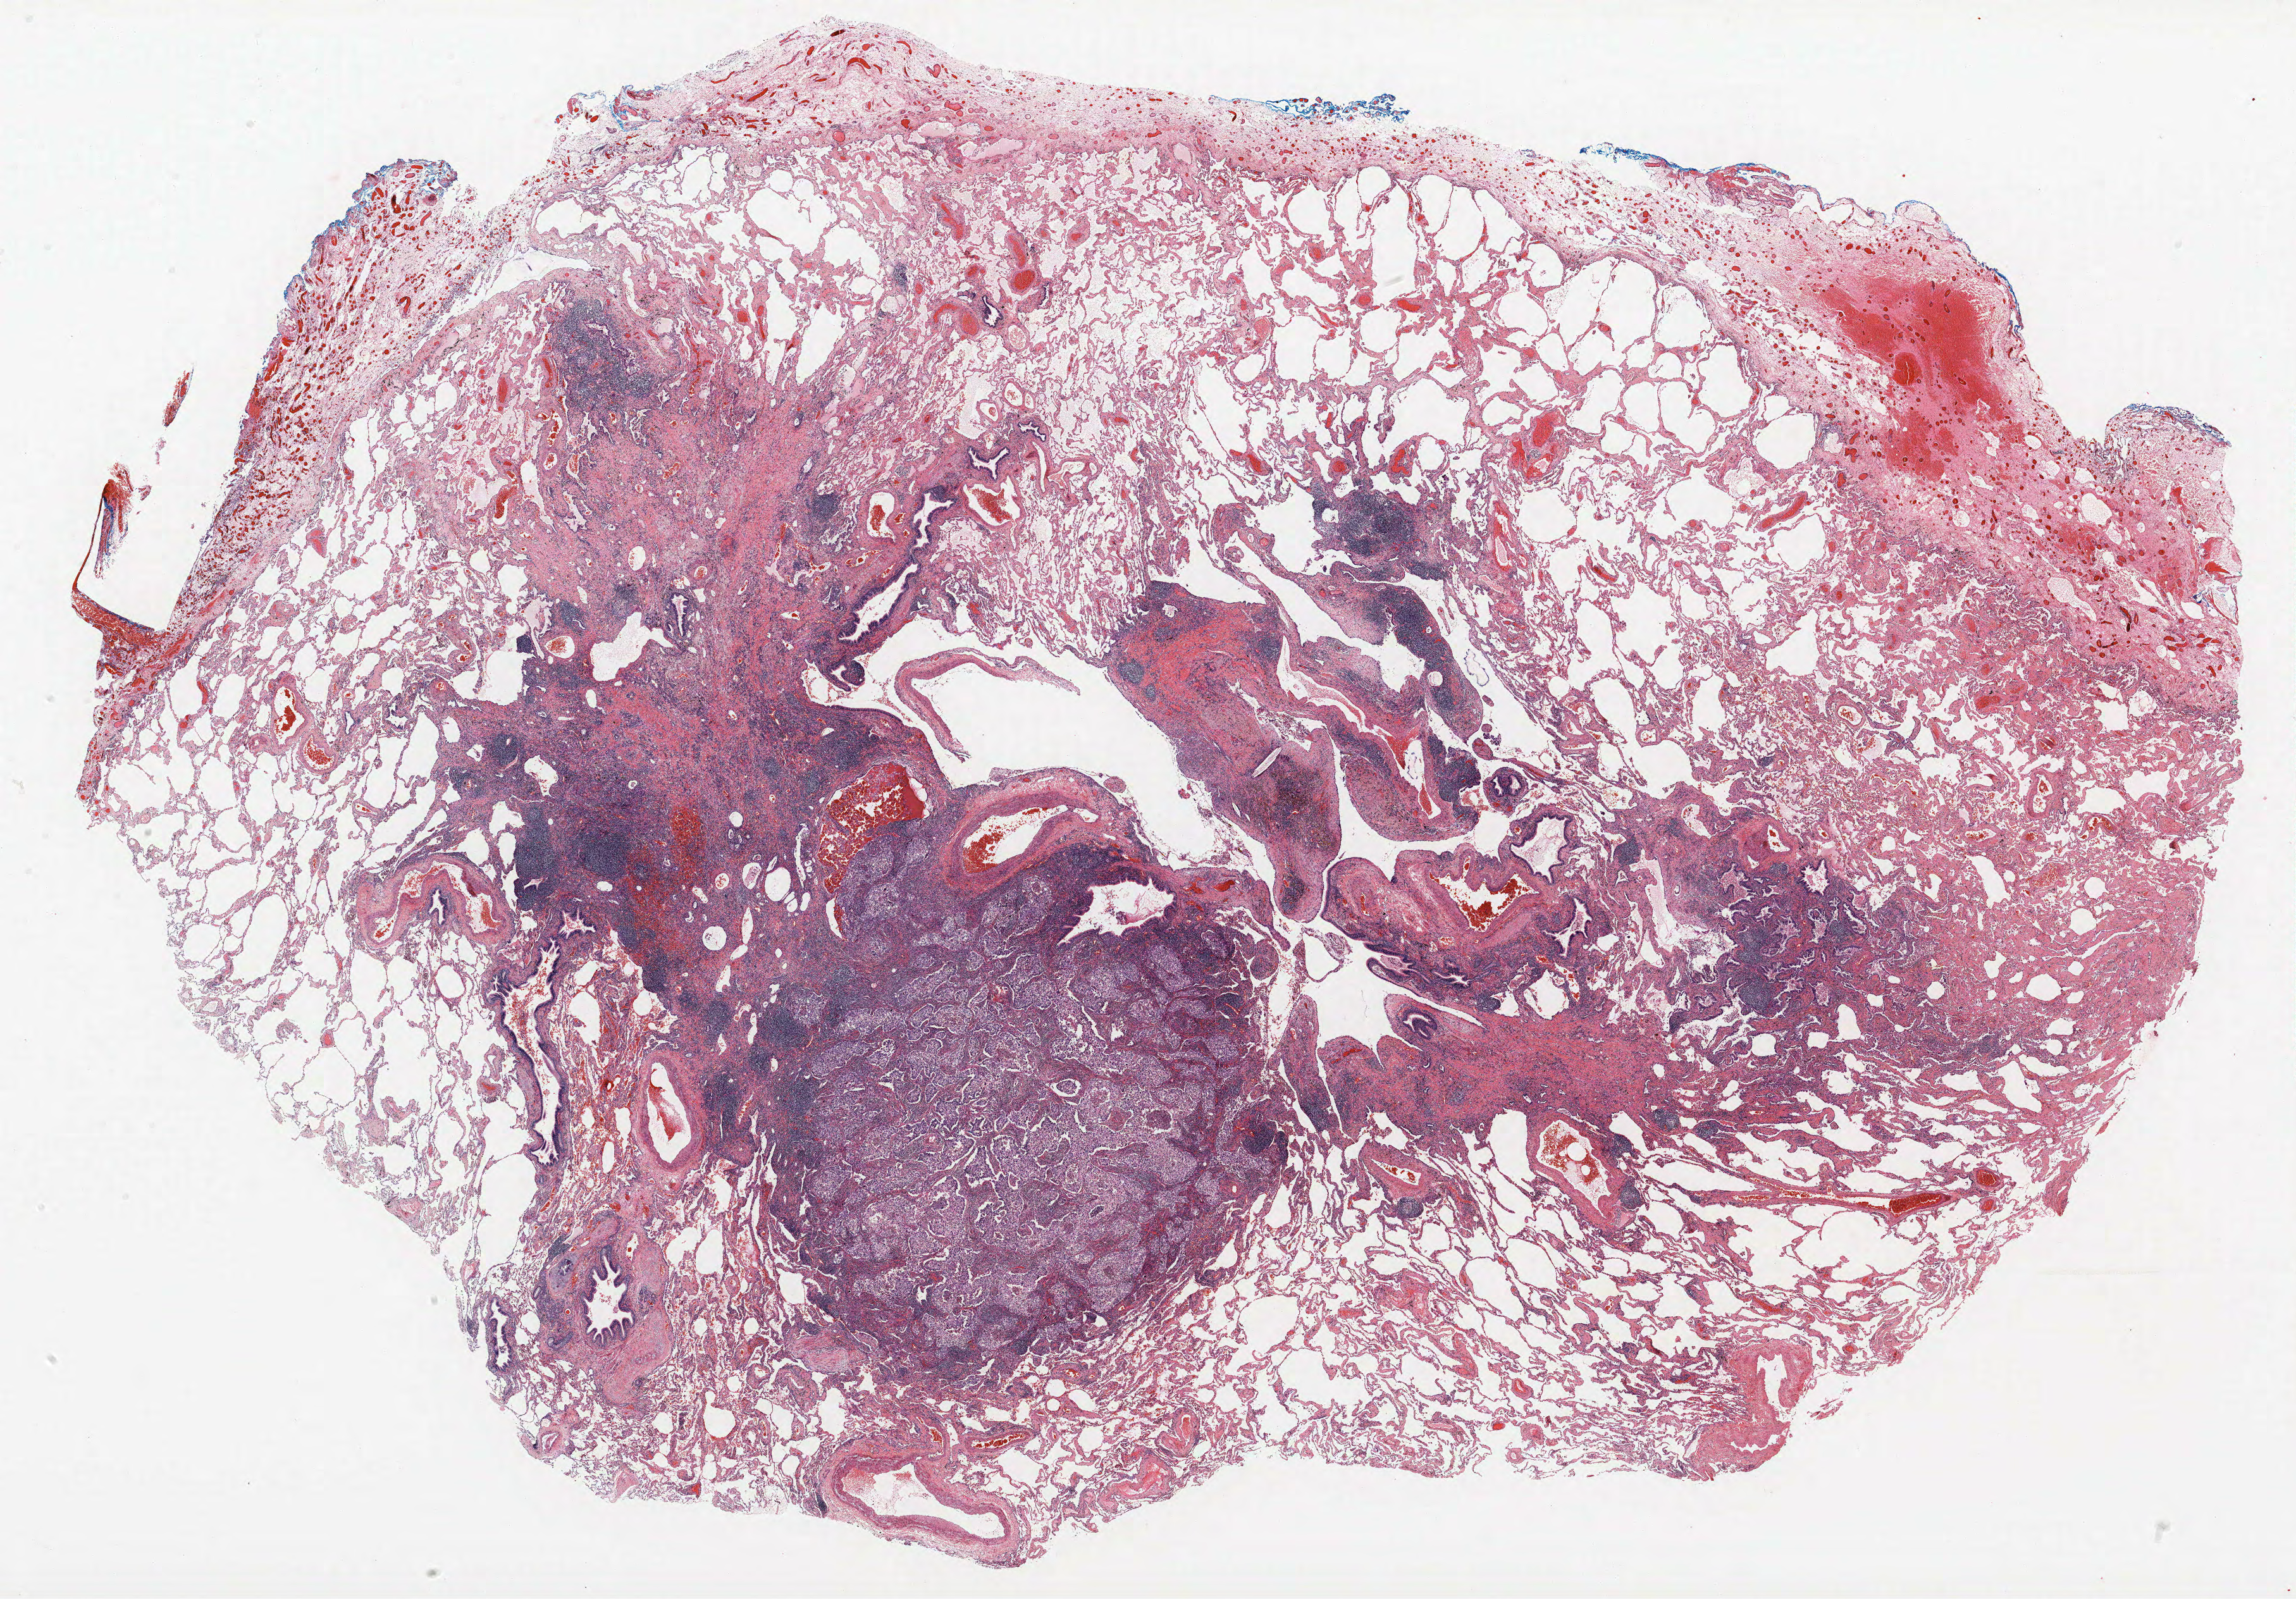
Hematoxylin and eosin (H&E) stained whole-slide image, a low-resolution overview of the entire scanned area, about 29.0 x 20.2 mm (slide scanned at 40x); FFPE section; lung tissue. Female, age 59 at enrolment. Current smoker at enrolment. Grade: poorly differentiated (G3).
* ICD-O-3 topography: lower lobe of lung (C34.3)
* stage (AJCC 6th edition): IA
* tumour size (pathology): 15 mm
* primary tumour location (clinical record): left lower lobe
* participant's lung-cancer diagnosis: Adenocarcinoma, NOS